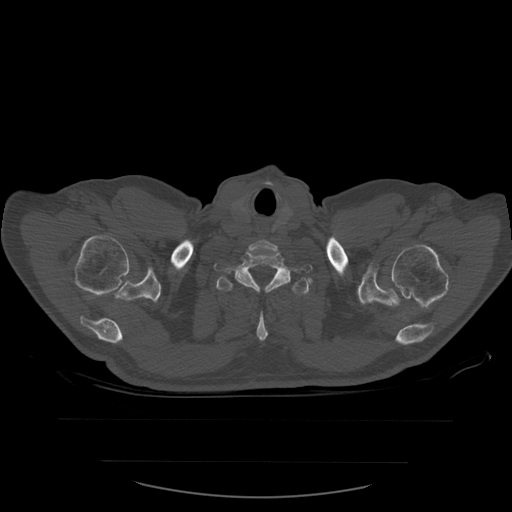
CT including the spine, one axial slice. Slice 486 of 590 in the series (ordered by position). Bone window (W 1800 / L 400 HU). 1.25 mm slice thickness. 512 × 512 image matrix, field of view 479 × 479 mm. Patient age 71 years. Case-level facts recorded for this patient, not image findings: primary cancer: lung; vertebrae with lytic lesions (as recorded): T1, T2, L5, S1.
Structures marked on this image (semi-automatic segmentation, software-assisted and operator-edited):
- T1 vertebra: bounding box [x1, y1, x2, y2] px = [214, 246, 313, 292]
- T2 vertebra: [216, 266, 312, 342]